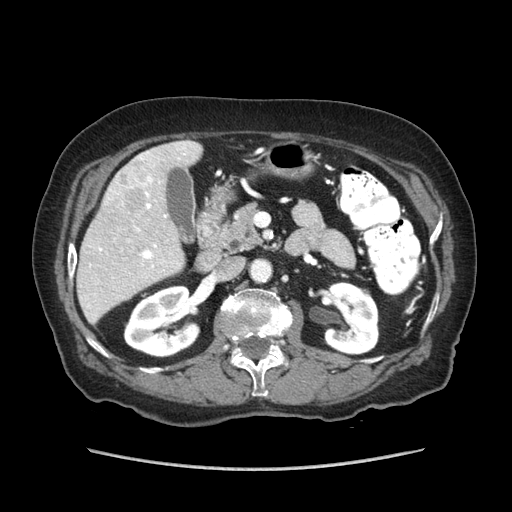
Contrast-enhanced abdominal CT (liver protocol), one axial slice; position 31 of 89 along the scan axis; reconstruction kernel STANDARD; soft-tissue window (W 400 / L 40 HU); 512 × 512 image matrix. From the clinical record (not read from this slice): diagnosis: hepatocellular carcinoma (patient treated with transarterial chemoembolisation; whether this scan precedes or follows treatment is not stated here); TNM stage (as recorded): Stage-IIIA; Child-Pugh class: A; tumour differentiation: well differentiated; tumour nodularity: multinodular.
Annotated regions visible in this slice (semi-automatically segmented with operator editing):
- liver parenchyma outside the tumour (the mass and vessels are separate outlines, so this box may not span the whole liver): bounding box <78,140,202,323> (left, top, right, bottom; pixels)
- mass: <104,159,150,210>
- liver vessels: <90,147,185,267>